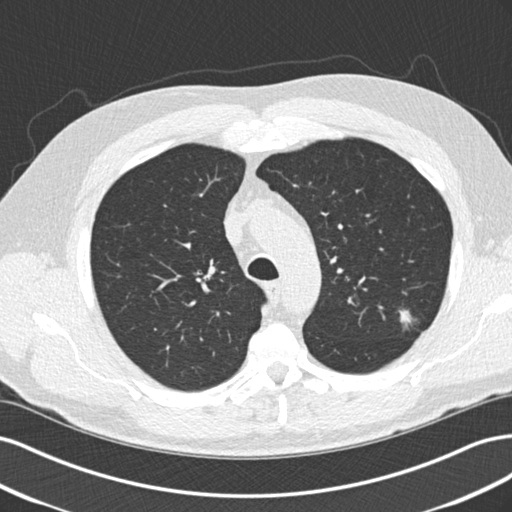
Chest CT (low-dose screening protocol), one axial image; second screening round (one year after baseline); lung window (W 1500 / L -600 HU); slice 51 of 209 in the series; 512 × 512 image matrix. Male, age 65 years at enrolment. Former smoker at enrolment.
Lesion marked by an expert reader, box from (x=388, y=305) to (x=425, y=340) px. Reader record for this screening exam (exam-level; its link to the box is not recorded): non-calcified nodule or mass ≥4 mm, left upper lobe, 10 × 9 mm, poorly defined margins, mixed attenuation, pre-existing on the prior screen: yes; interval growth: no. Official screen result: positive, other. Participant outcome: lung cancer diagnosed 221 days after this screen — adenocarcinoma, NOS, left upper lobe, poorly differentiated (G3), stage IA (AJCC 6th edition), 13 mm at pathology.